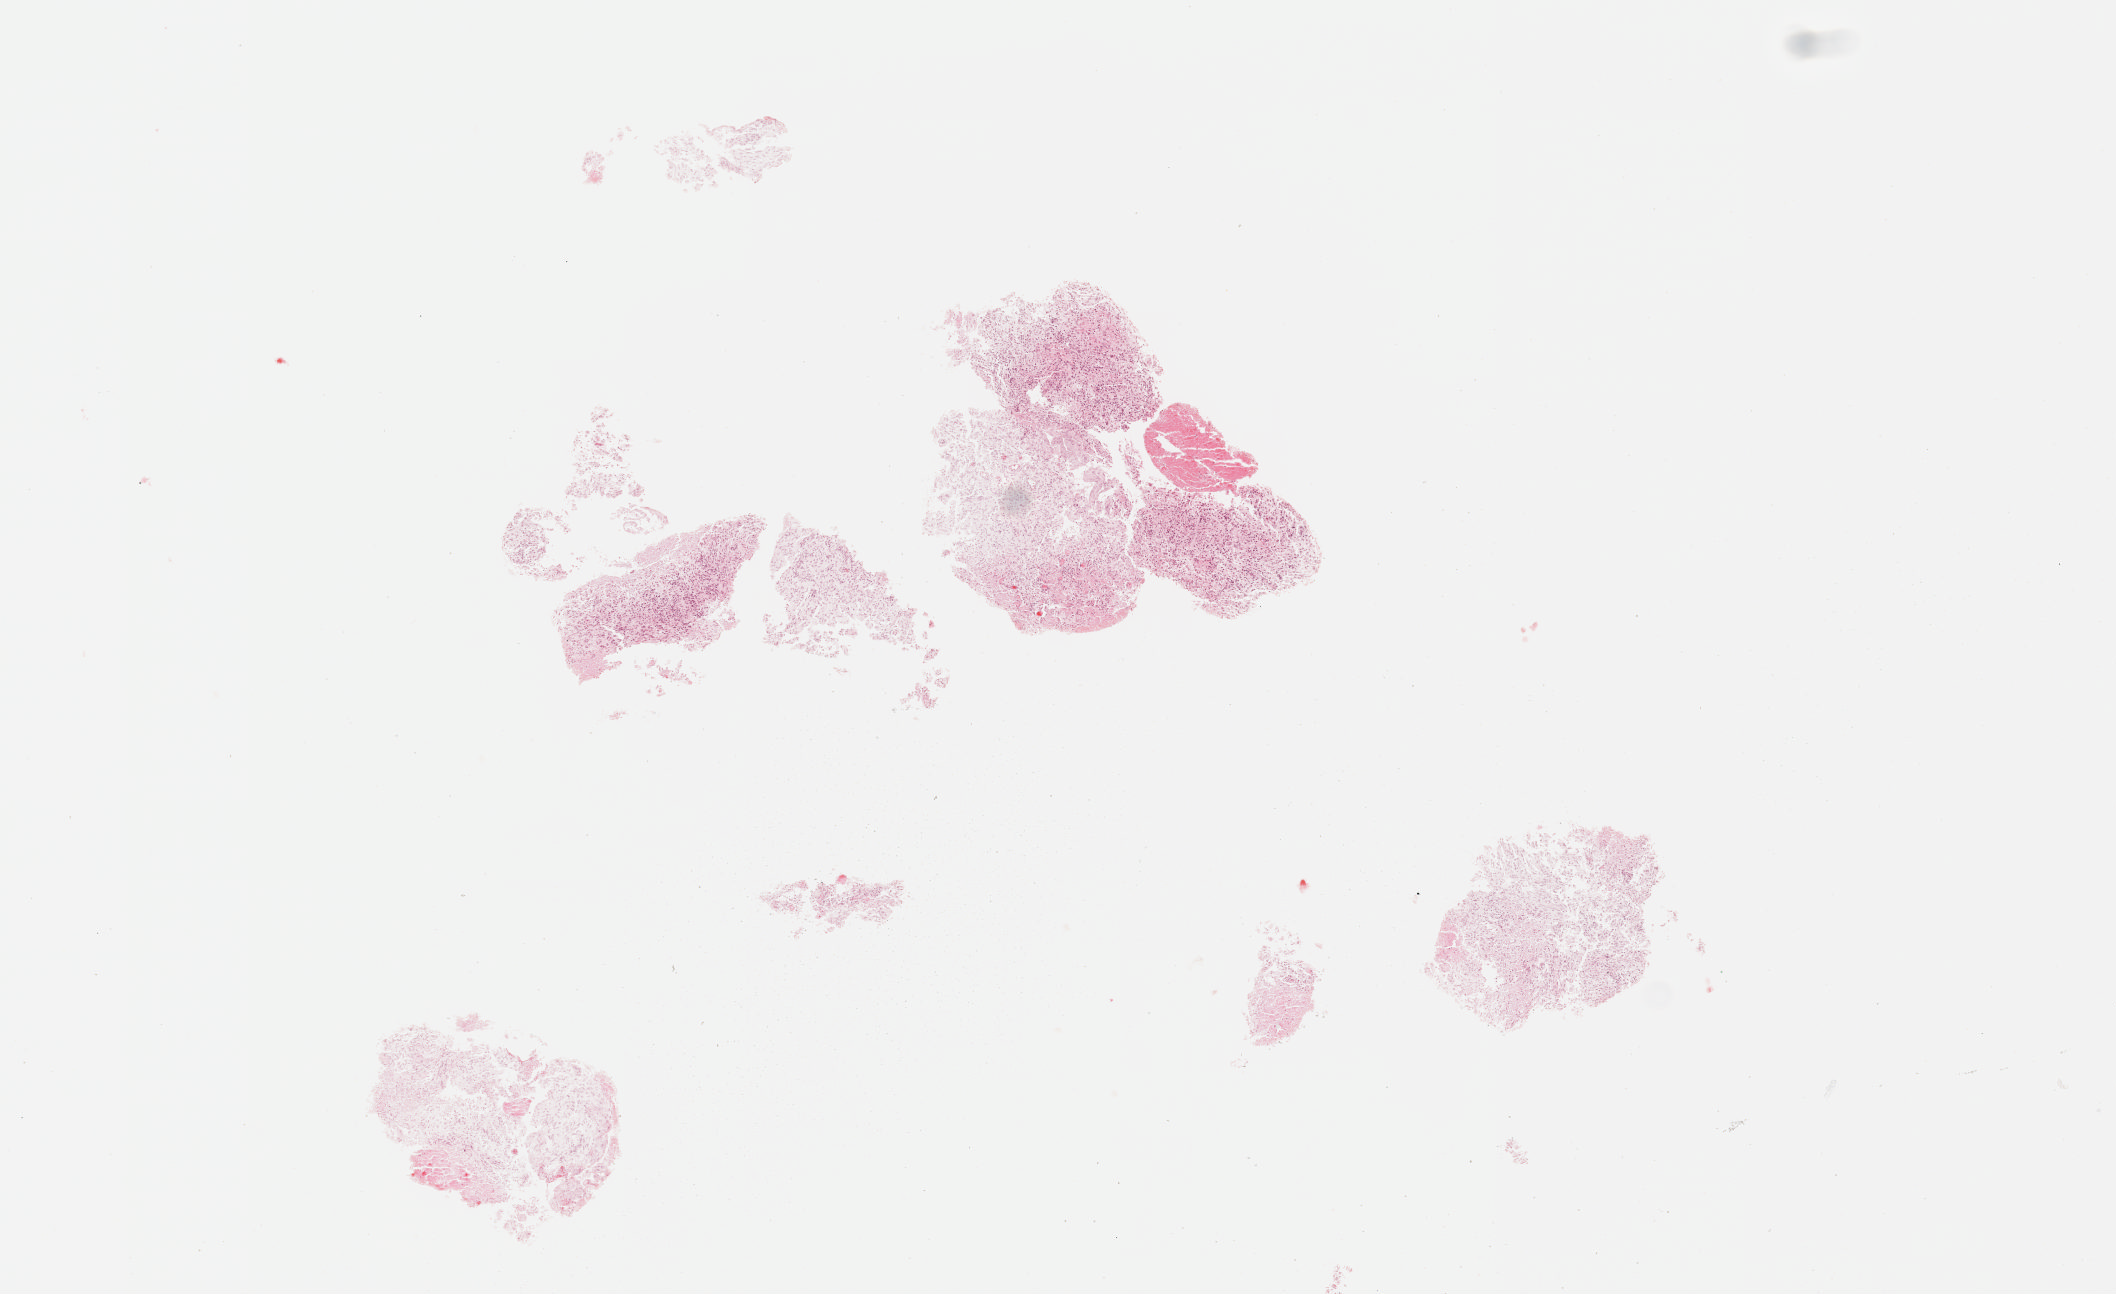
H&E whole-slide image, whole scanned area (about 8.6 x 5.2 mm, from a 40x scan) shown as a low-resolution overview; FFPE section; sample: primary tumour, brain. Patient: male, age at initial diagnosis 63 years.
- diagnosis: Glioblastoma